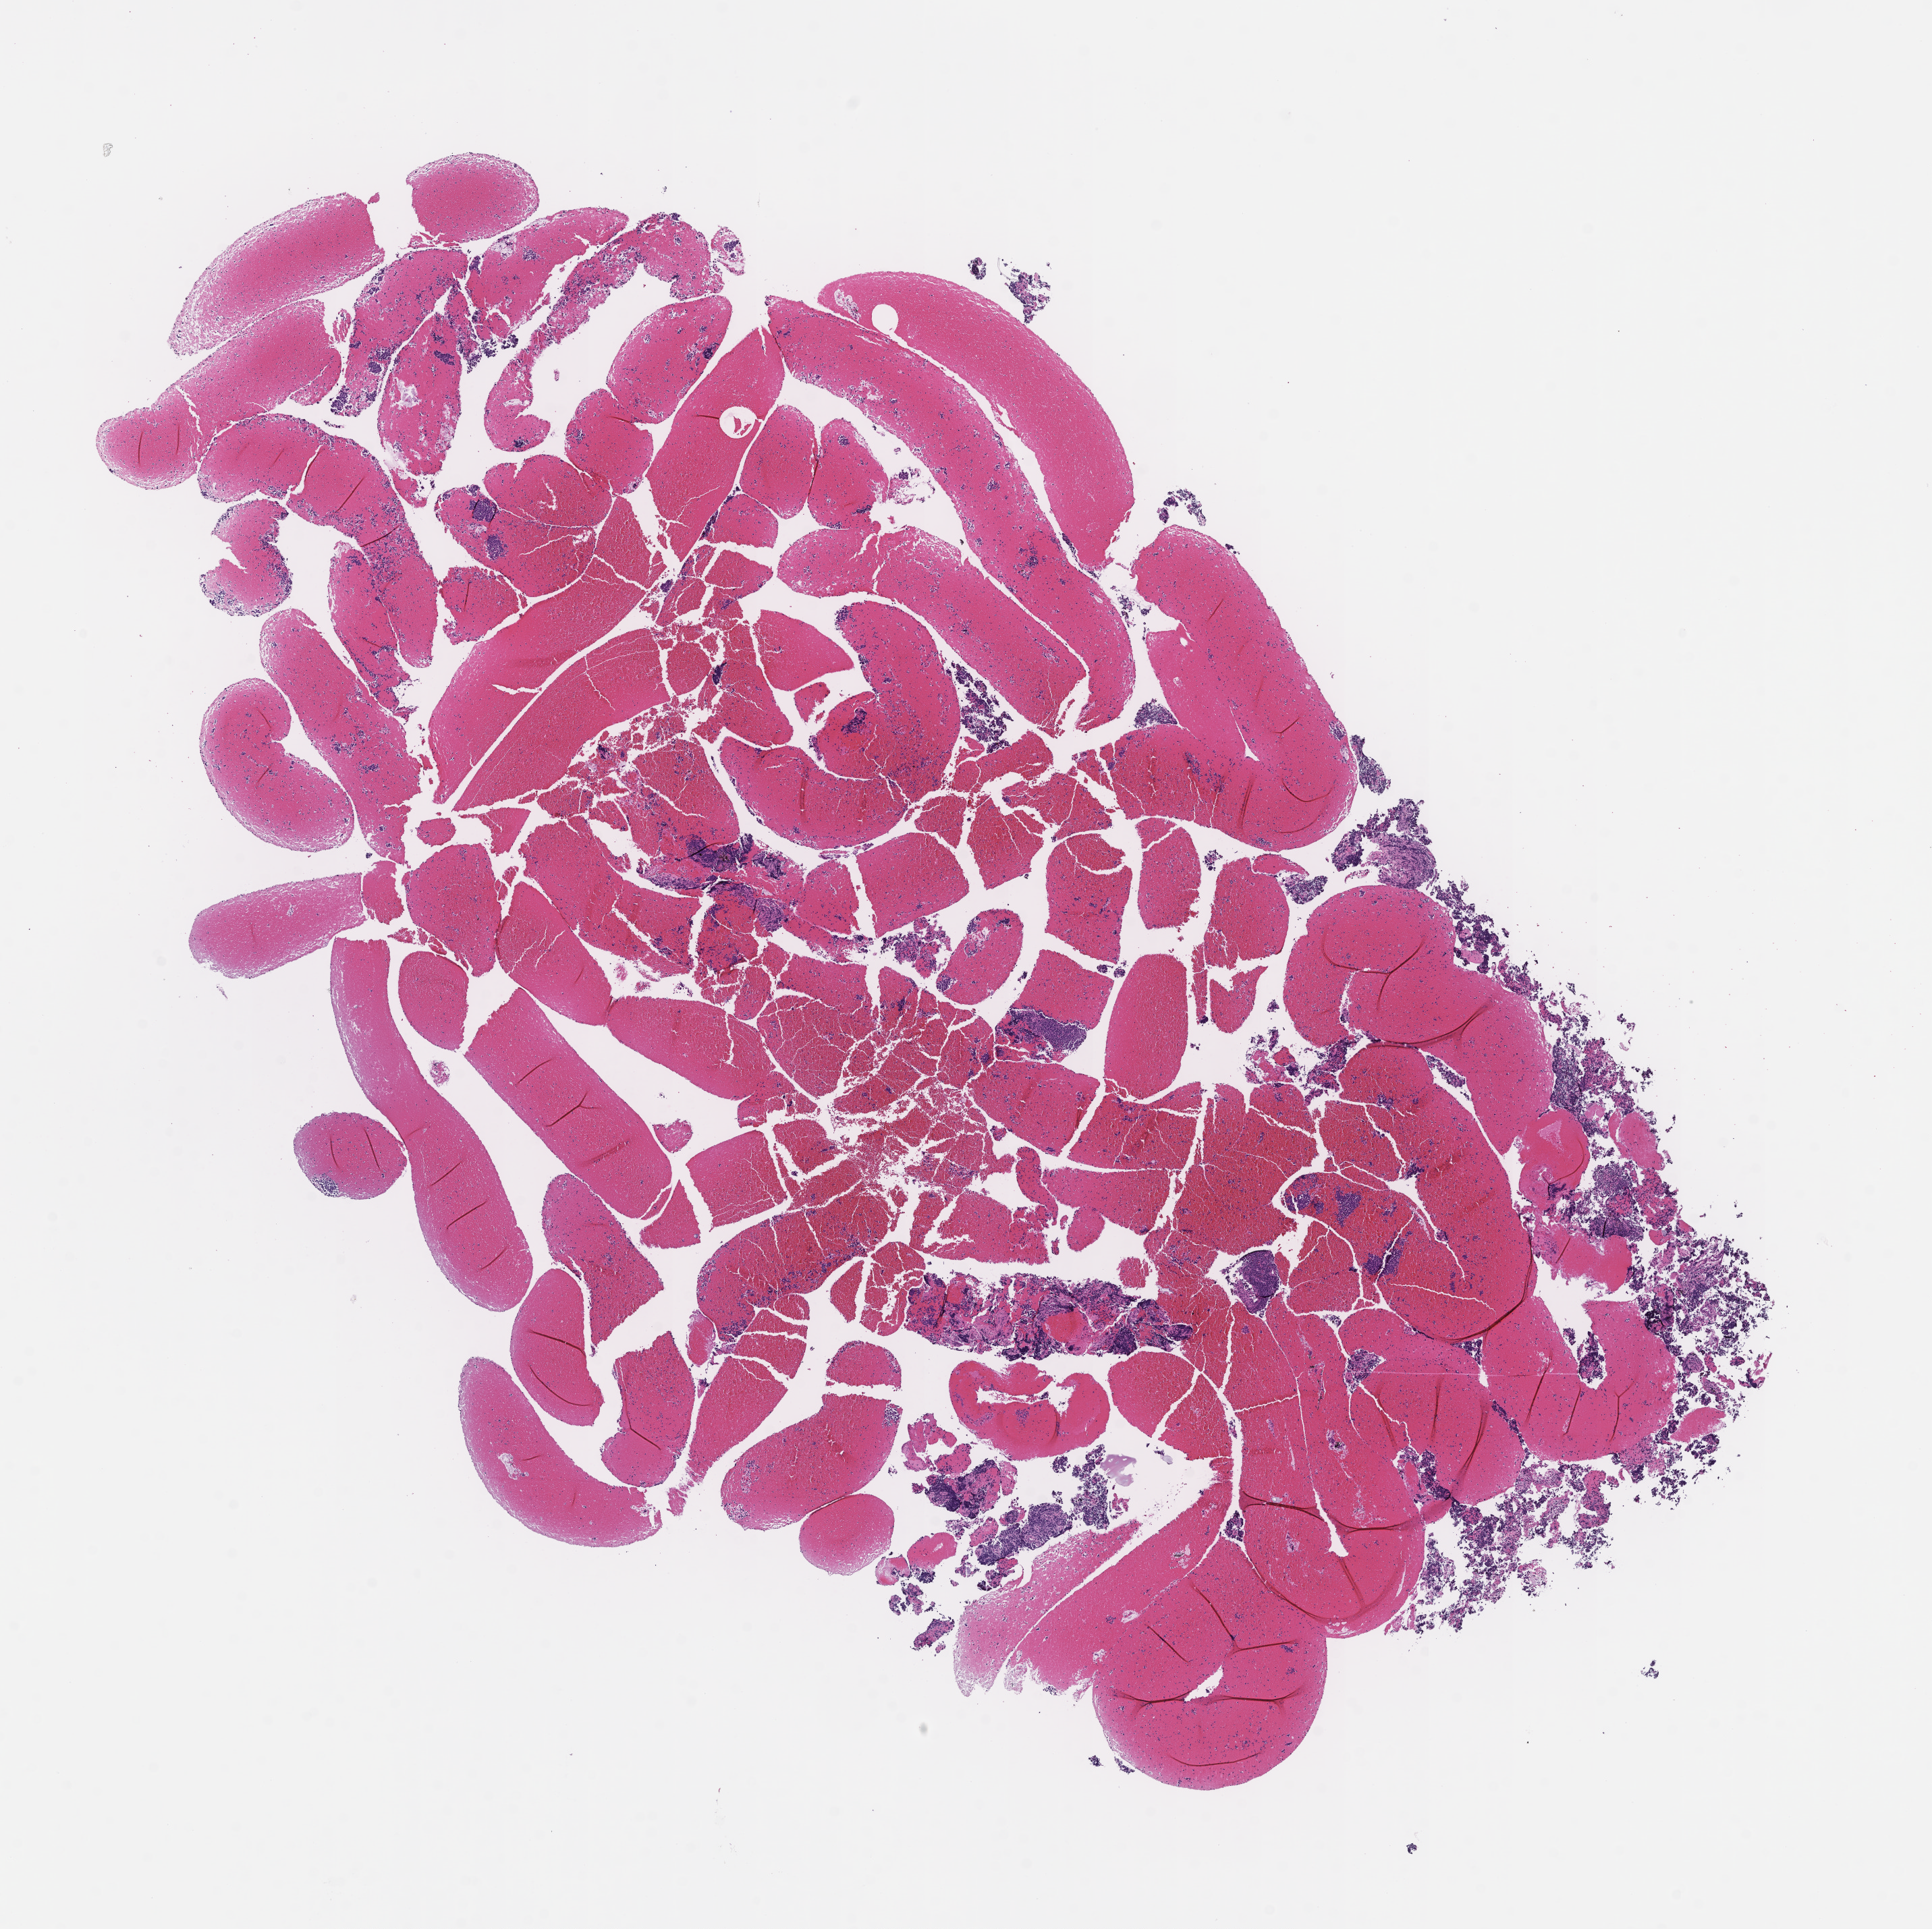
Whole-slide image, H&E stain, shown as a low-resolution overview of the whole scanned area (about 11.6 x 11.5 mm), formalin-fixed paraffin-embedded section, tissue site: lung. Patient: male.
- this section: primary tumor
- diagnosis: Small Cell Lung Carcinoma